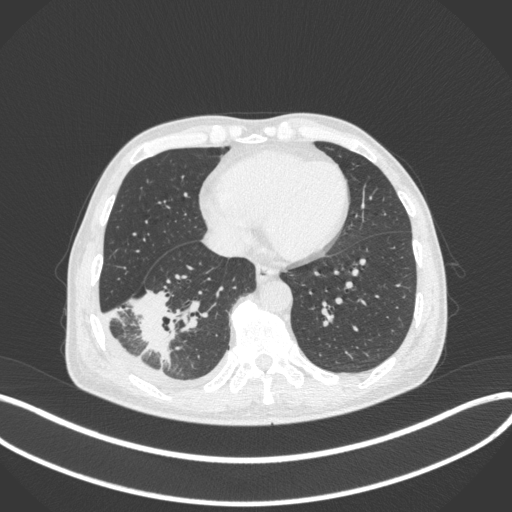
Chest CT, one axial slice. Position 124 of 385 along the scan axis. Reconstruction kernel B31f. 120 kVp. Lung window (W 1500 / L -600 HU). 1 mm slice thickness. 512 × 512 image matrix, field of view 400 × 400 mm. Patient: male, 64 years. From the clinical record (not read from this slice): clinical TNM (as recorded): T3 N0 M0; histopathological grade: G2-3.
Outlined on this slice (bounding box drawn by a radiologist):
- lung tumour (recorded histology: adenocarcinoma): bounding box <126,281,174,370> (left, top, right, bottom; pixels)